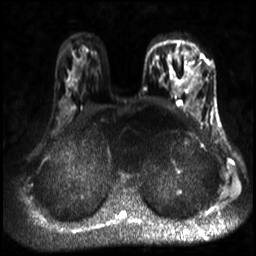
Breast MRI, one axial slice; position 21 of 30 along the scan axis; diffusion-weighted series; image 2 of 4 stored at this slice position (different b-values; order by instance number); 3 T; 256 × 256 image matrix, field of view 320 × 320 mm. Female patient.
Annotated regions visible in this slice (manually delineated by an expert):
- tumour on diffusion-weighted imaging: box from (x=186, y=48) to (x=200, y=92) px